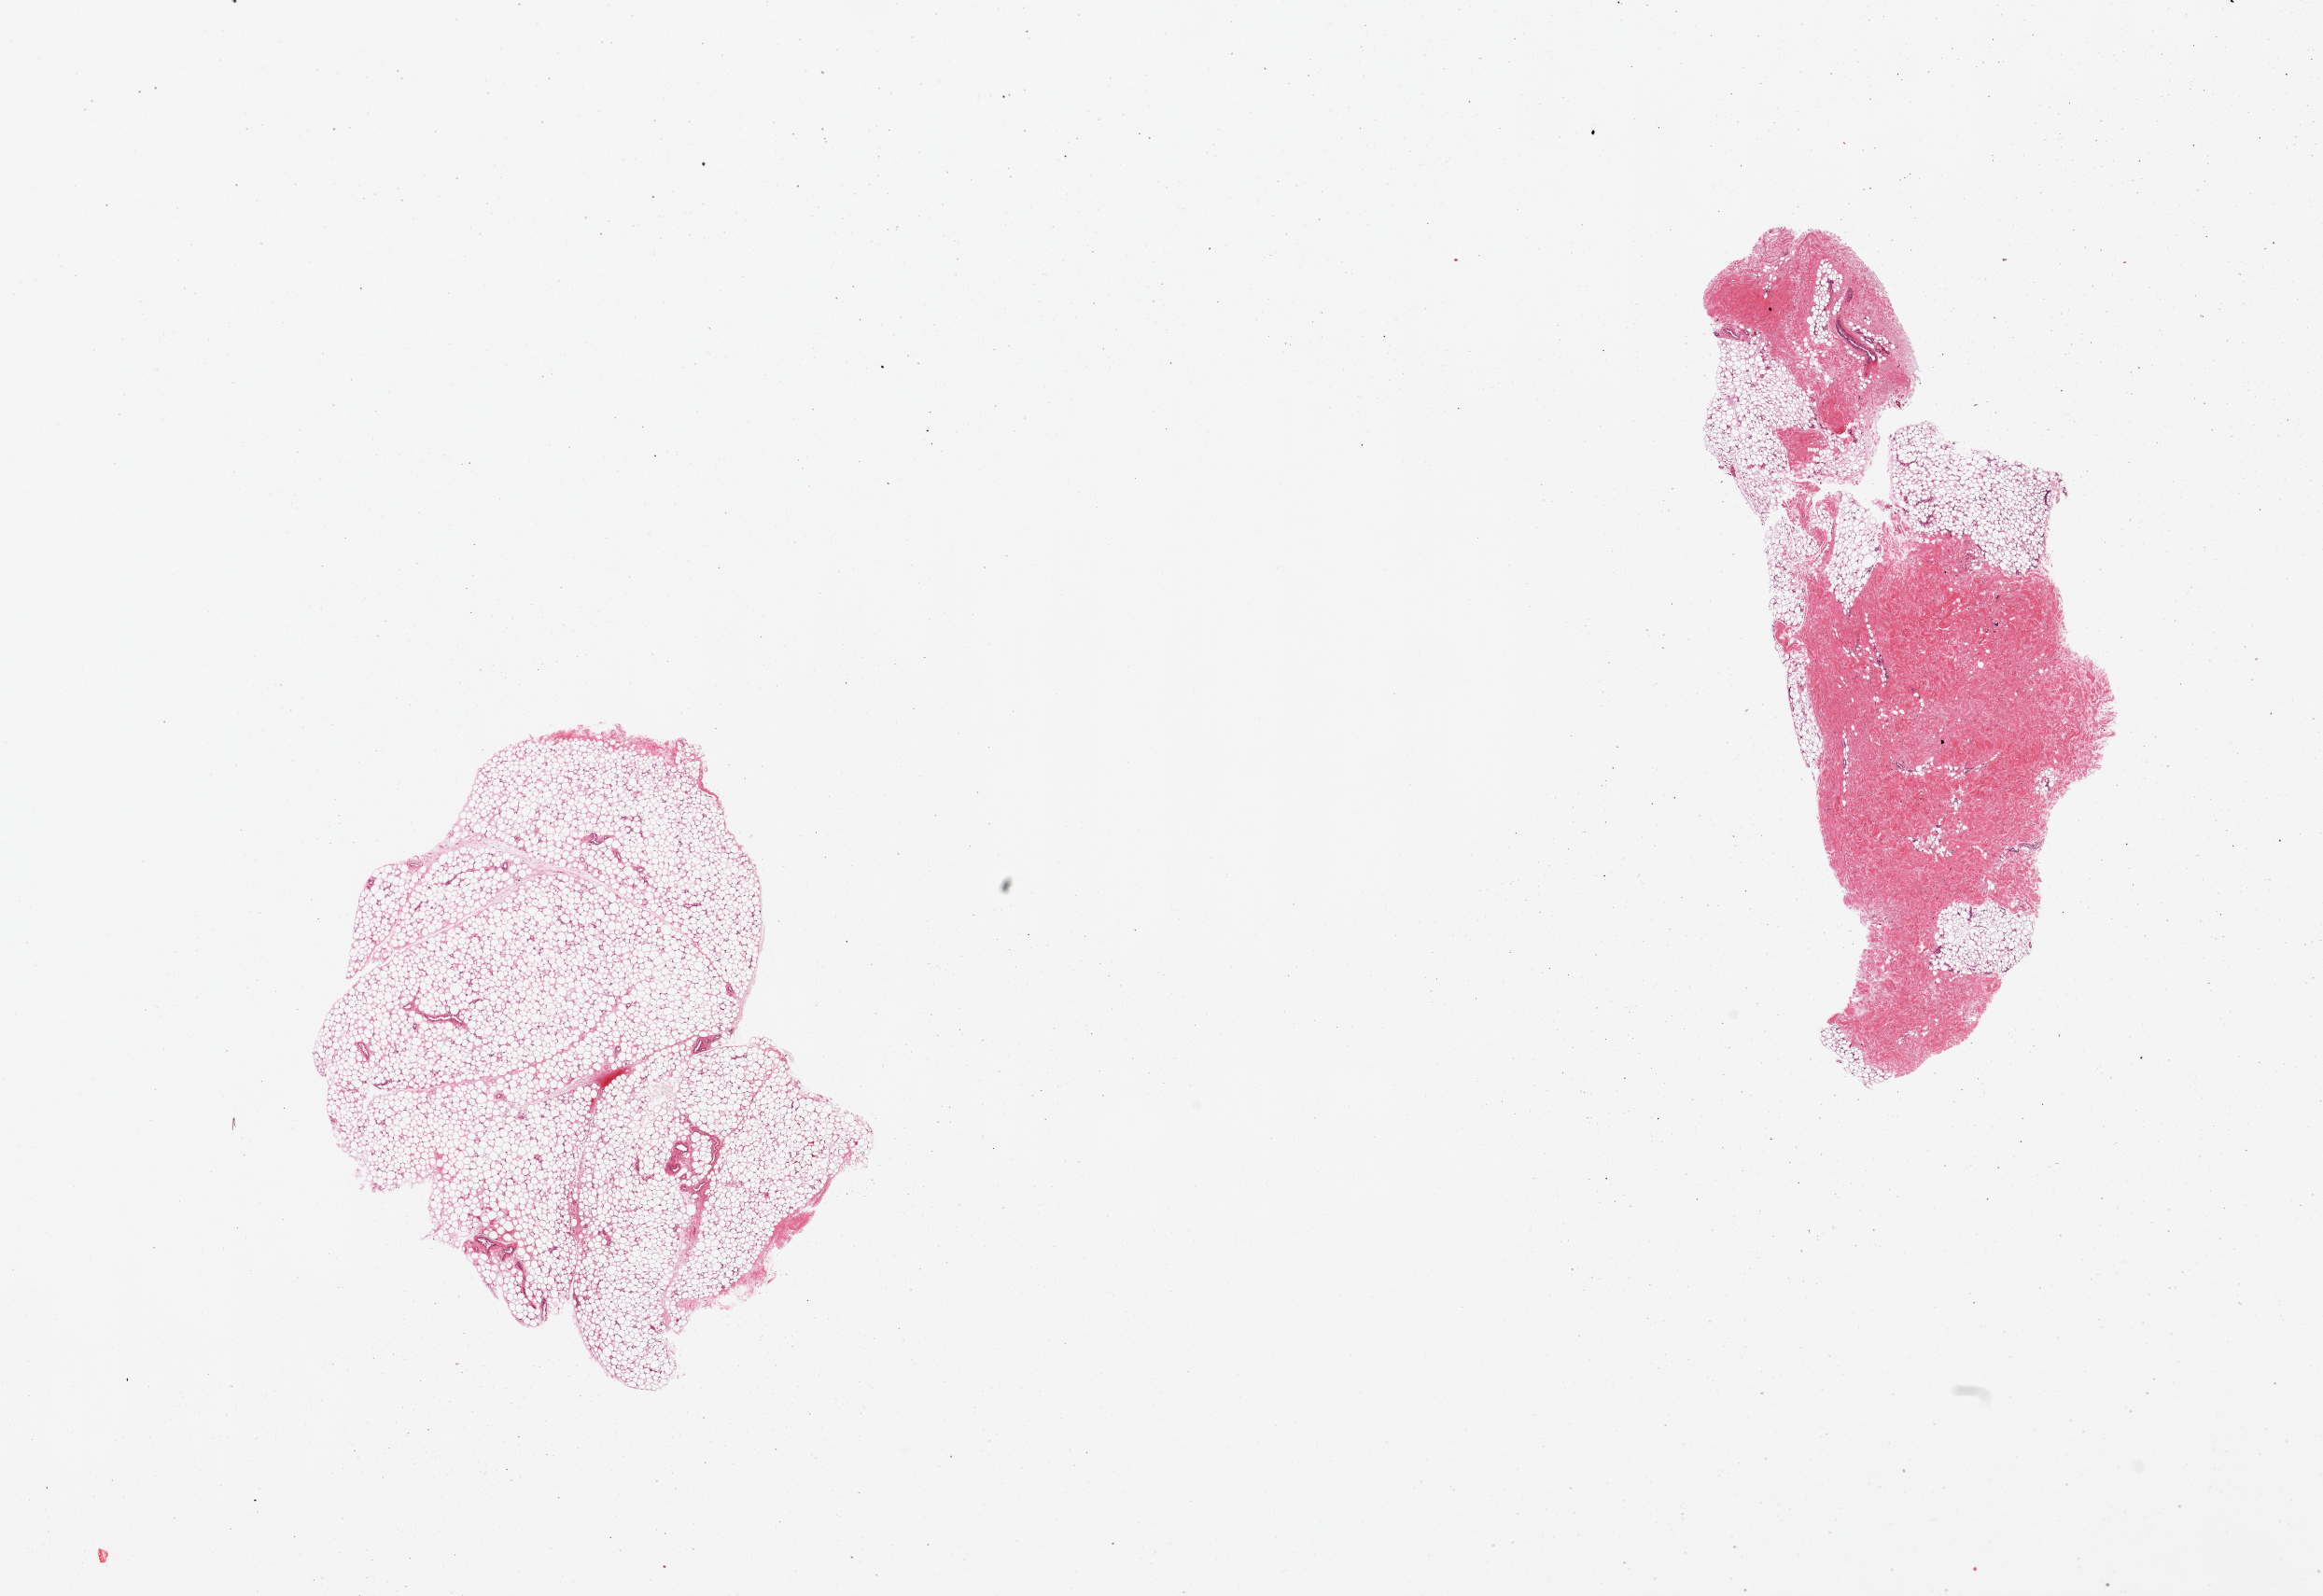
Whole-slide image, haematoxylin and eosin stain, whole scanned area (about 19.7 x 13.5 mm, slide scanned at 20x) shown as a low-resolution overview. PAXgene-fixed, paraffin-embedded tissue. Sampled site (target tissue): breast. Tissue donor sample.
Reviewer comment on this tissue sample: 2 pieces; 1 fibrous, other fatty; no mammary ducts.